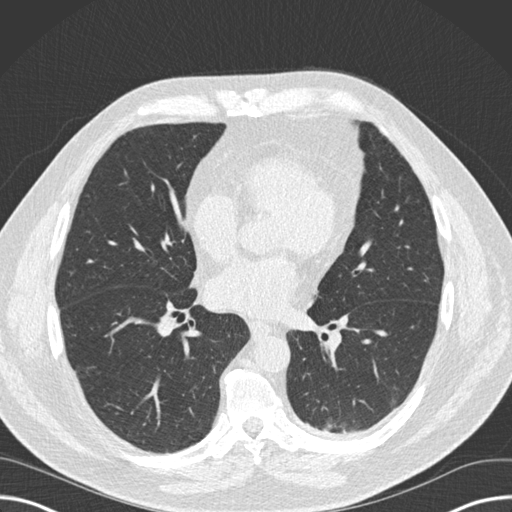
Low-dose screening chest CT, one axial slice. Slice 74 of 160 in the series (ordered by position). Lung window (W 1500 / L -600 HU). 2 mm slice thickness. 512 × 512 image matrix, field of view 382 × 382 mm.
Outlined on this slice (manually delineated by an expert):
- lesion 1 (tumor, upper lobe of left lung): bounding box <344,431,346,433> (left, top, right, bottom; pixels)